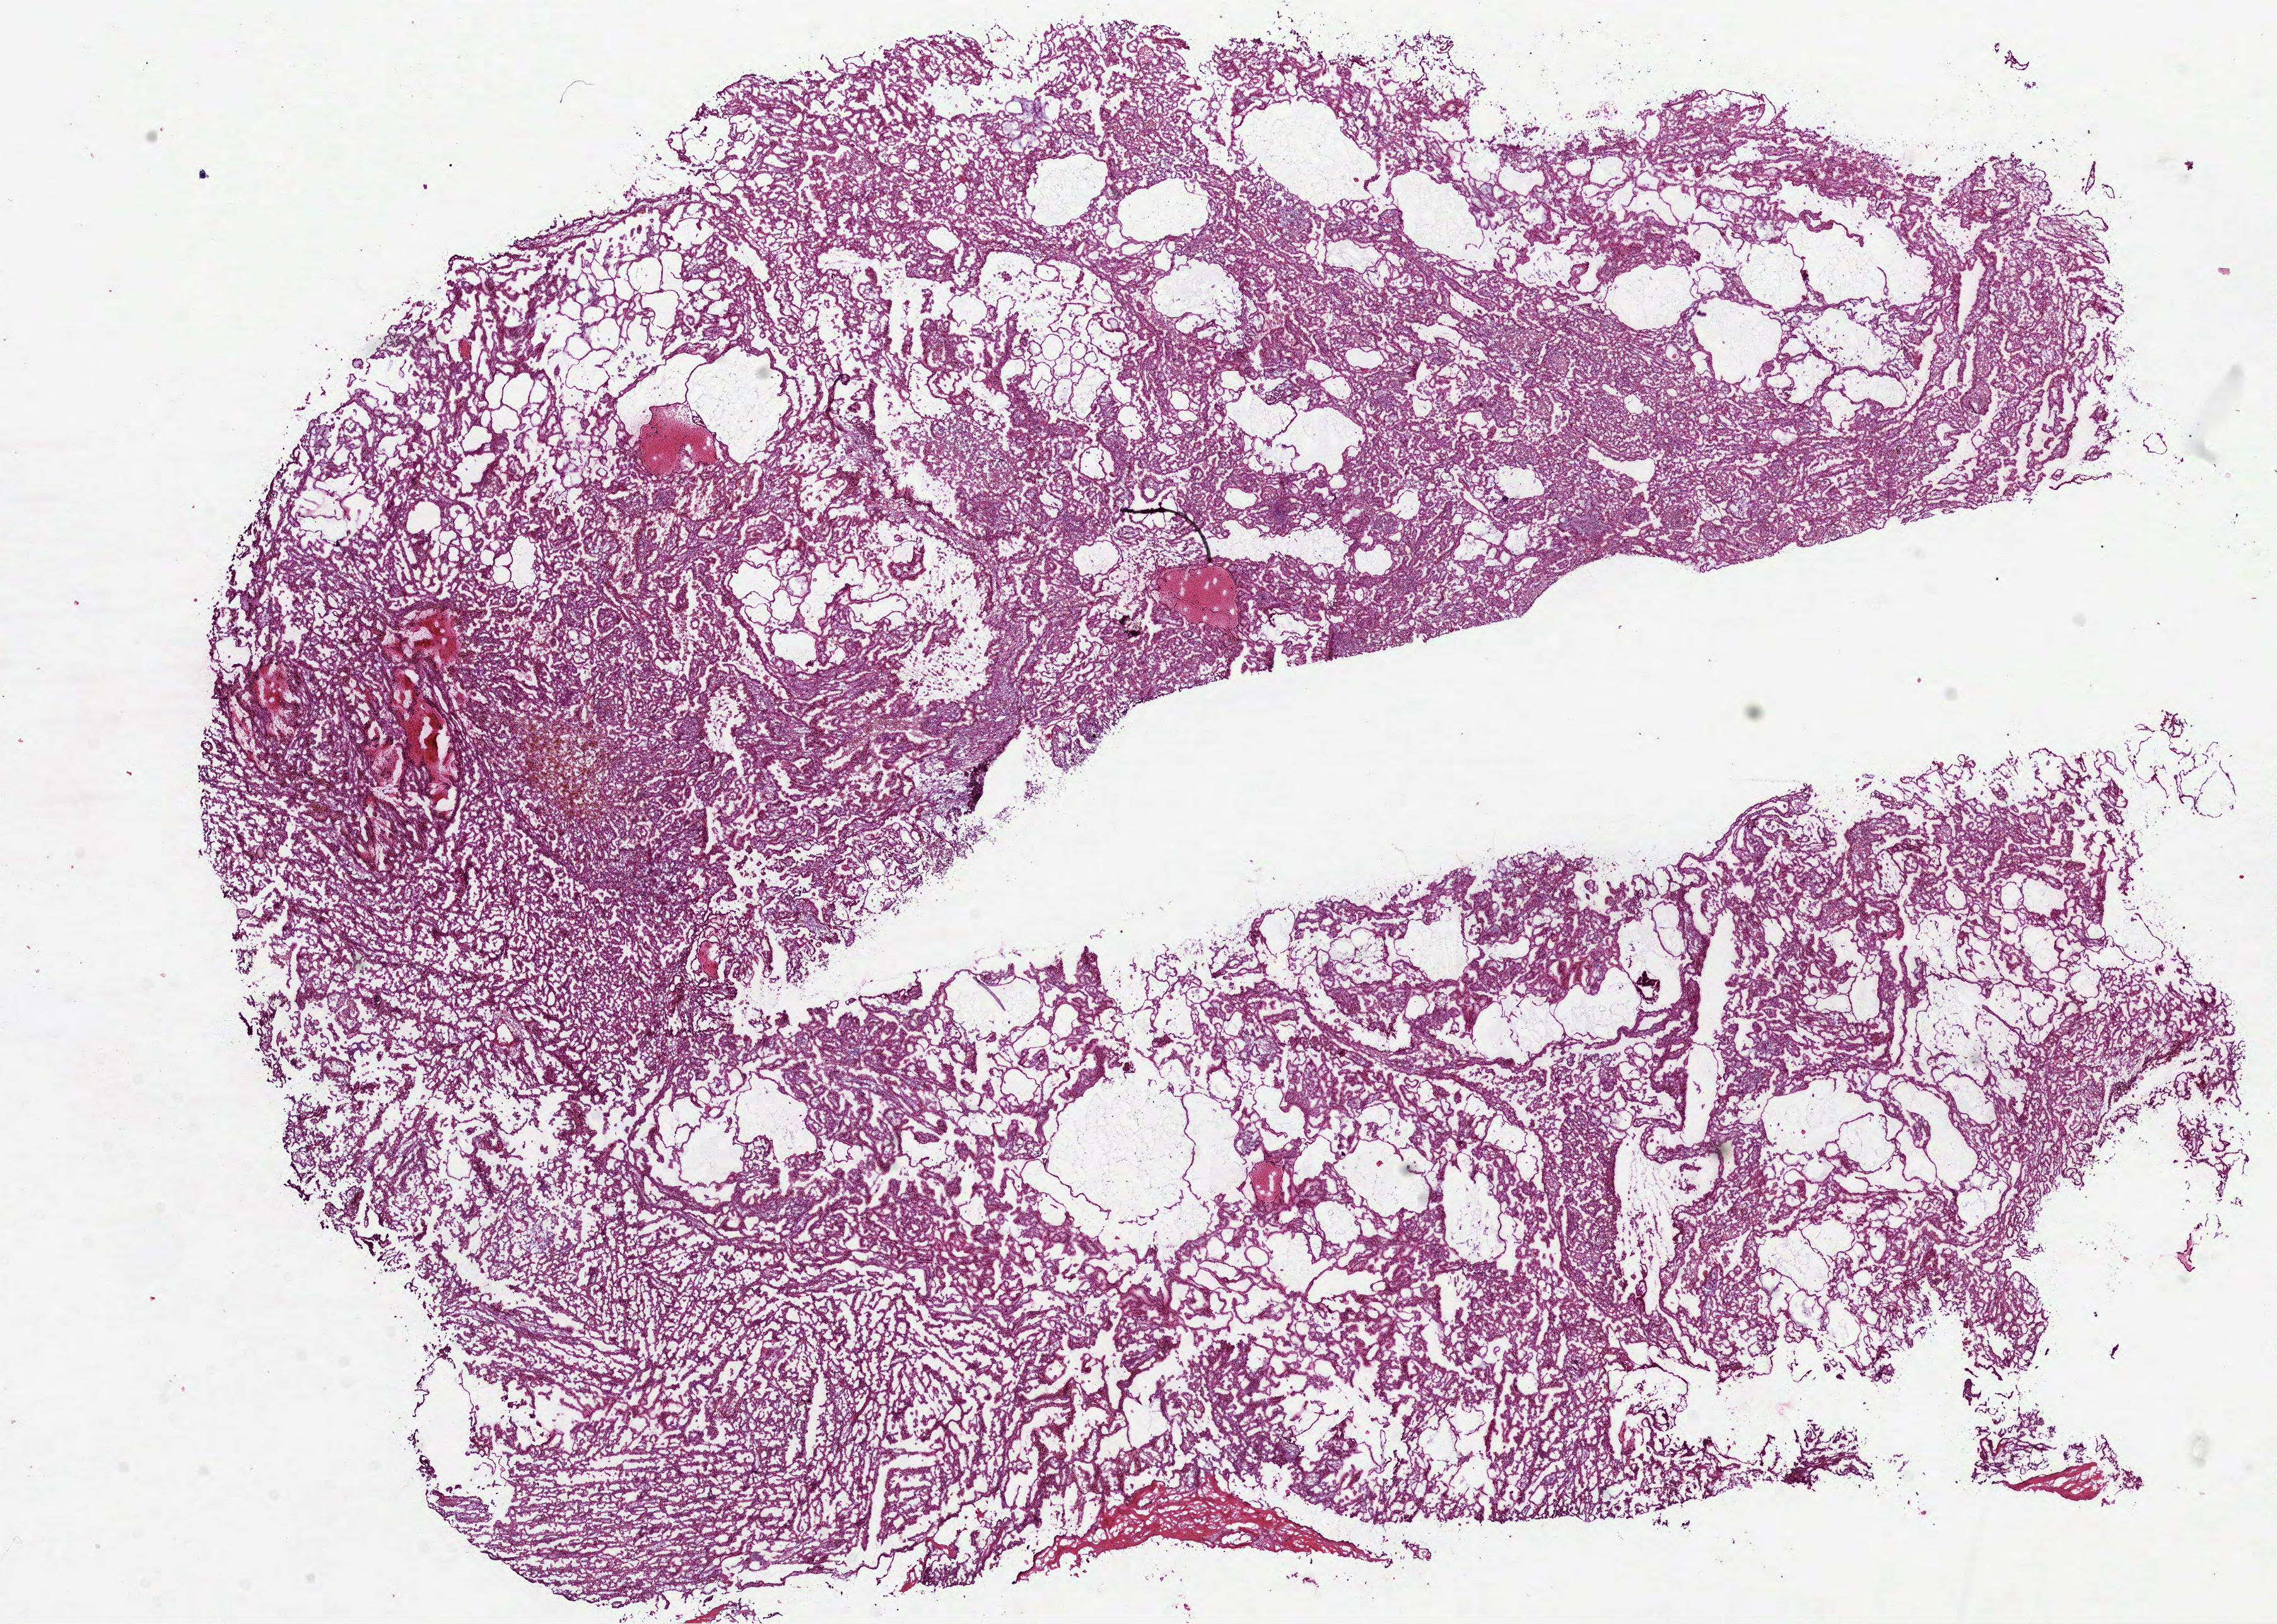
Digitized Hematoxylin and eosin (H&E) stained tissue section (whole slide), whole scanned area (about 14.6 x 10.4 mm, acquisition: 40x scan) shown as a low-resolution overview, frozen section from the top of the tissue portion, sample: primary tumour, kidney. Patient: male, age at initial diagnosis 42 years. Pathologist review of this section (percent, as recorded): tumour cells 85%, tumour nuclei 75%, normal cells 0%, stromal cells 15%, necrosis 0%.
Diagnosis: Papillary adenocarcinoma, NOS. AJCC pathologic stage: I (6th edition). TNM: T1 N0 M0.